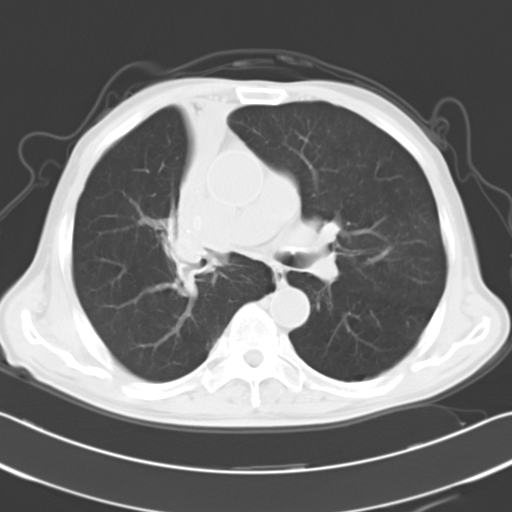
Chest CT, one axial slice; position 19 of 31 along the scan axis; 120 kVp; lung window (W 1500 / L -600 HU); 10 mm slice thickness; 512 × 512 image matrix, field of view 339 × 339 mm. Patient: male, 73 years. Case-level facts recorded for this patient, not image findings: clinical TNM (as recorded): T2a N1 M0.
Annotated regions visible in this slice (rectangle marked by the reading radiologist):
- lung tumour (recorded histology: squamous cell carcinoma): box from (x=170, y=83) to (x=219, y=244) px